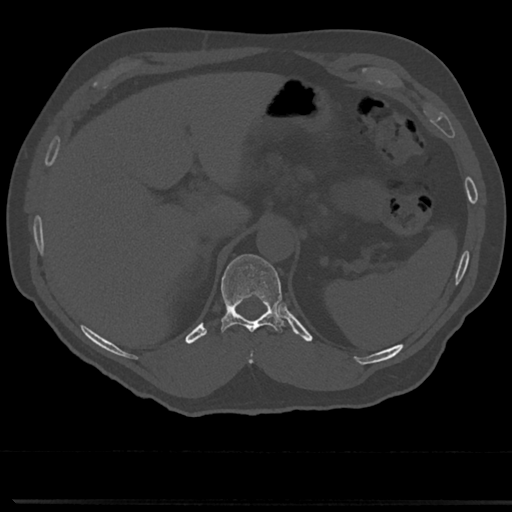
CT including the spine, one axial slice; position 205 of 817 along the scan axis; reconstruction kernel Br40s/3; 120 kVp; bone window (W 1800 / L 400 HU); 0.5 mm slice thickness; 512 × 512 image matrix, field of view 355 × 355 mm. Male patient, age 61 years. From the clinical record (not read from this slice): primary cancer: prostate.
Annotated regions visible in this slice (semi-automatic segmentation, software-assisted and operator-edited):
- T10 vertebra: box from (x=246, y=347) to (x=256, y=365) px
- T11 vertebra: (x=214, y=255)–(x=289, y=335)